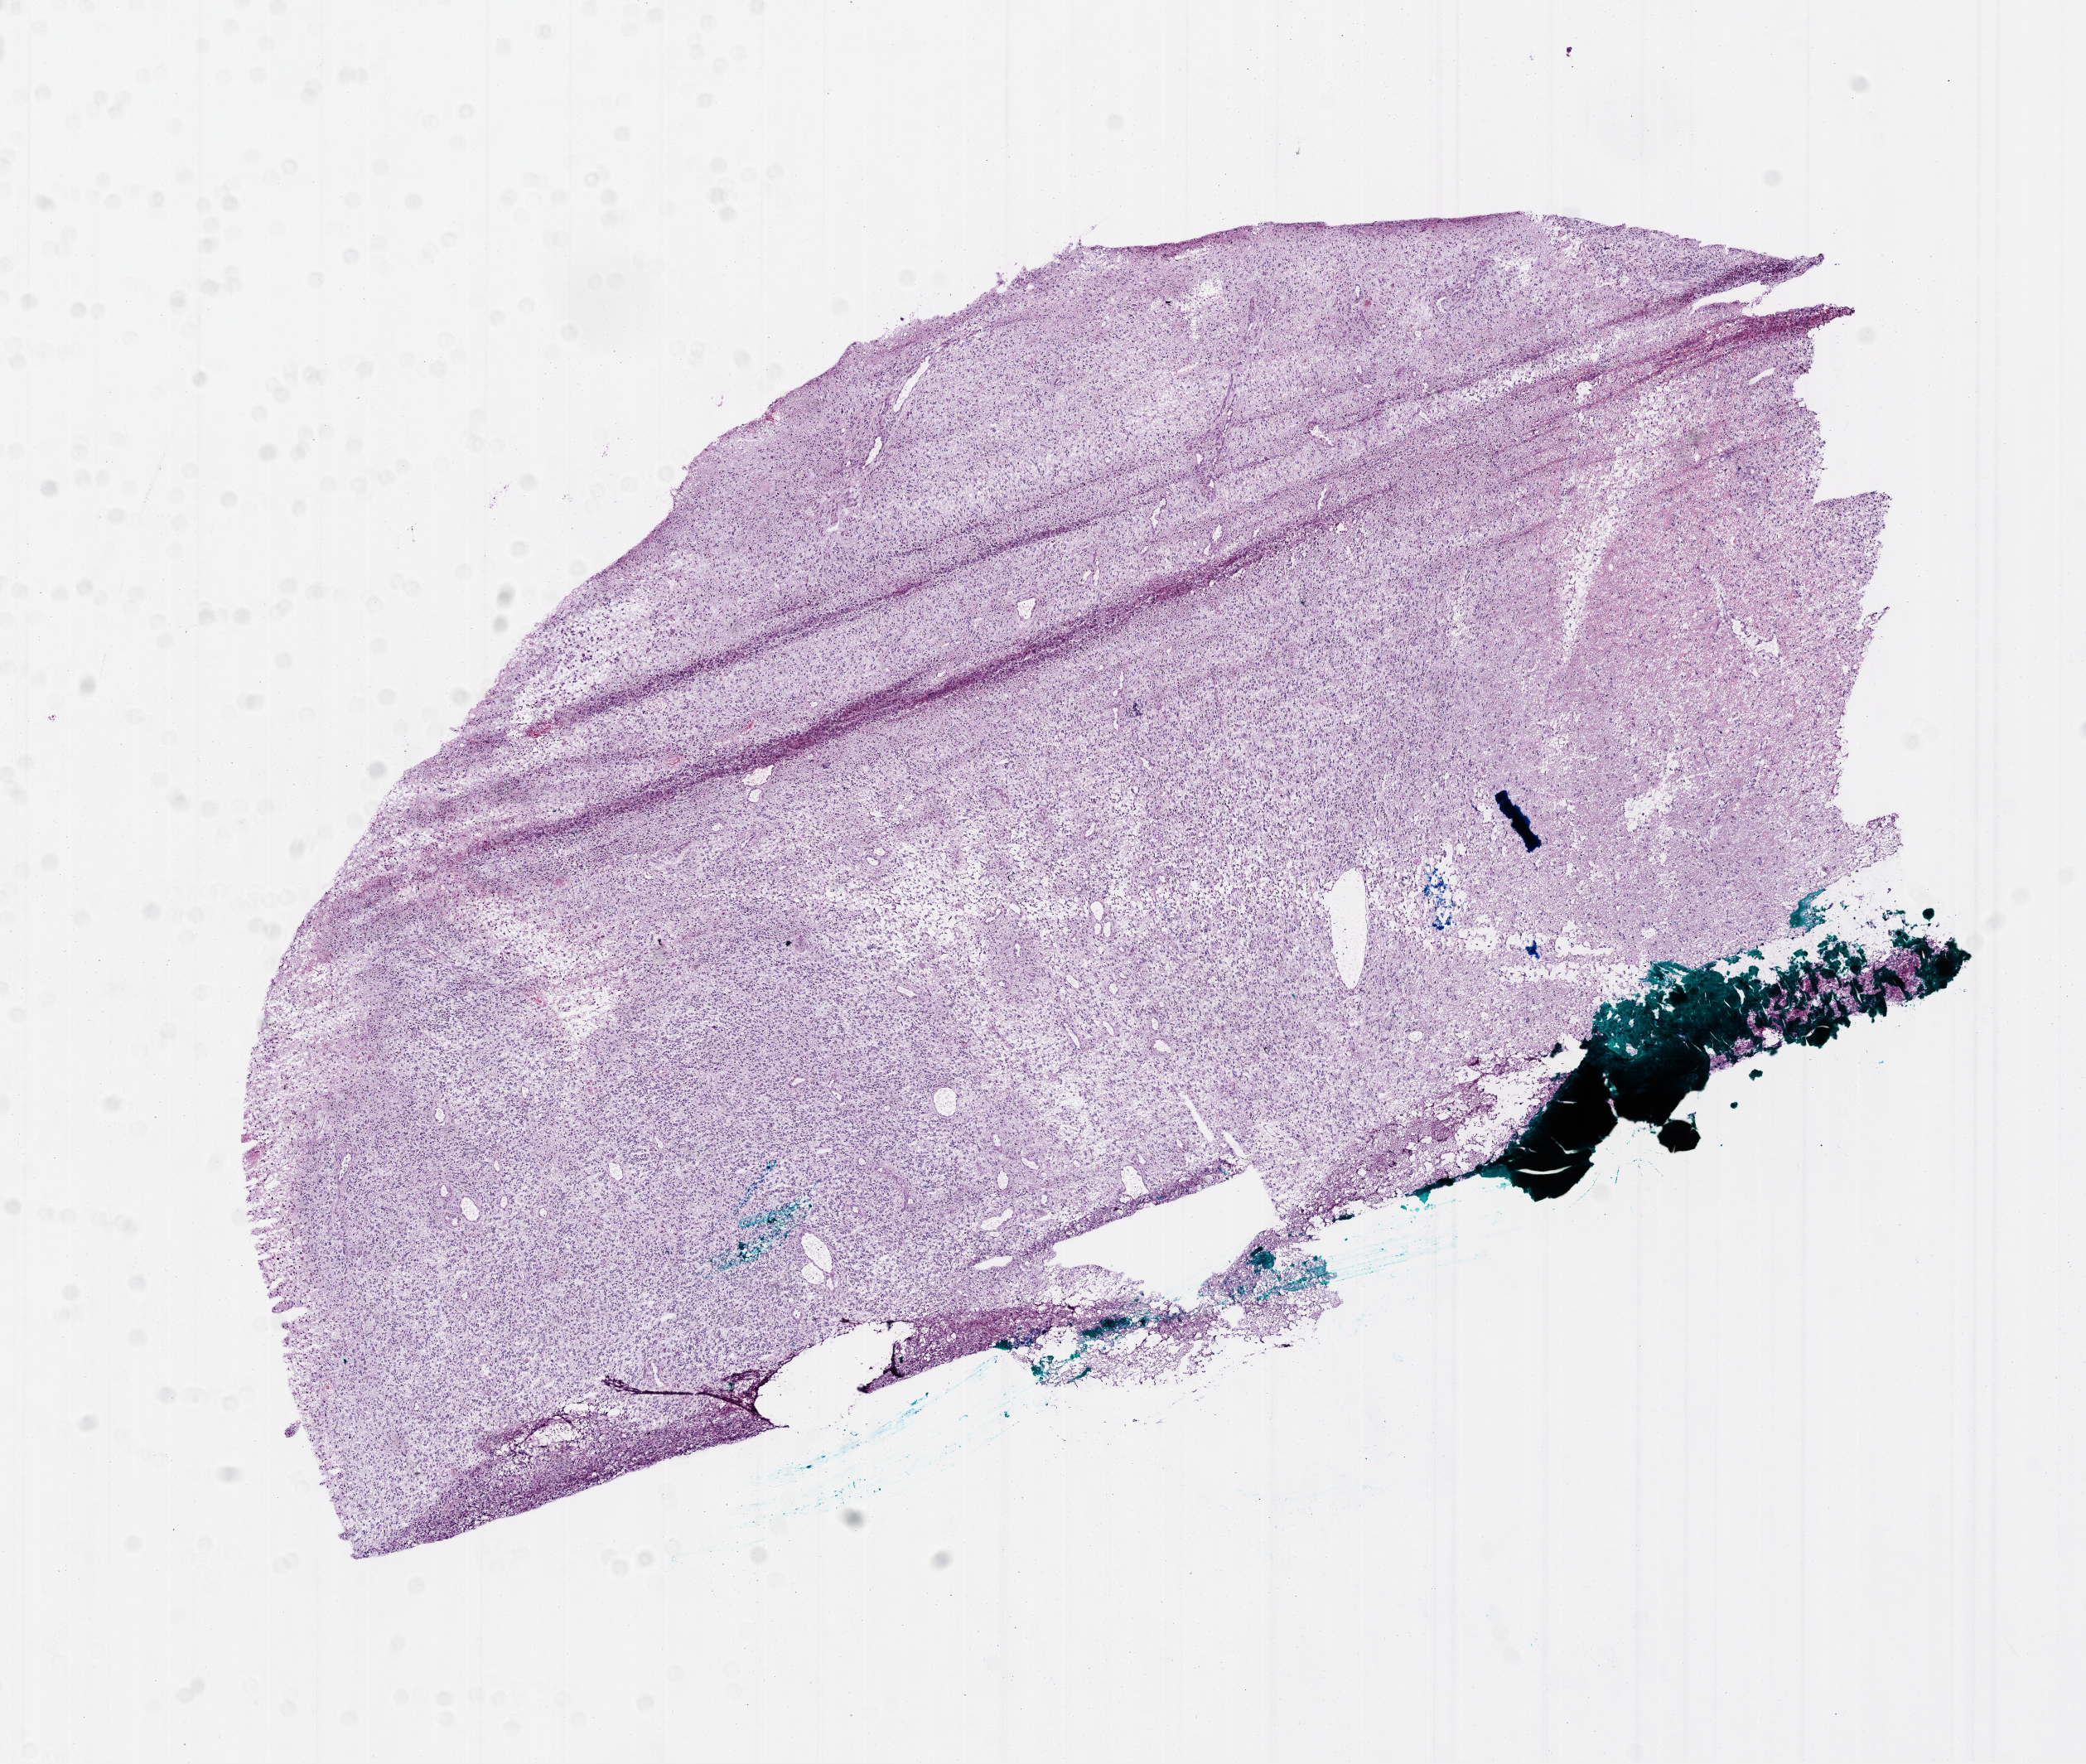
H&E-stained whole-slide image, a low-resolution overview of the entire scanned area, about 10.2 x 8.6 mm (from a 20x scan); frozen section; primary tumour sample from the brain. Female patient; age at initial diagnosis 76 years. Slide review estimates, as recorded: tumour cells 85%, tumour nuclei 90%, normal cells 0%, stromal cells 10%, necrosis 5%.
Pathologic diagnosis: Glioblastoma.